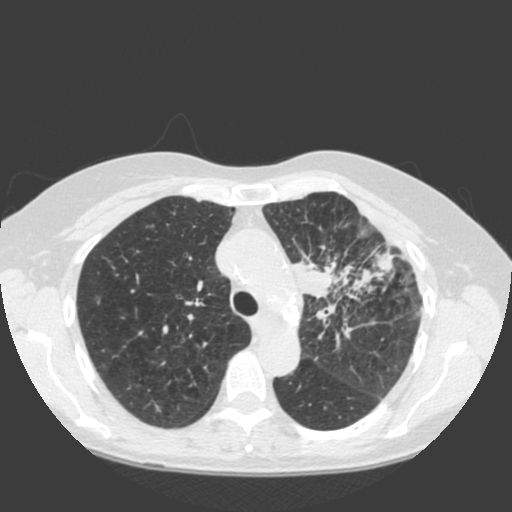
Low-dose screening chest CT, one axial slice. Slice 137 of 184 in the series (ordered by position). 120 kVp. Lung window (W 1500 / L -600 HU). 2 mm slice thickness. 512 × 512 image matrix, field of view 350 × 350 mm.
Annotated regions visible in this slice (manually delineated by an expert):
- lesion 1 (tumor, hilum of left lung): bounding box (x1, y1, x2, y2) in pixels: (290, 242, 395, 327)